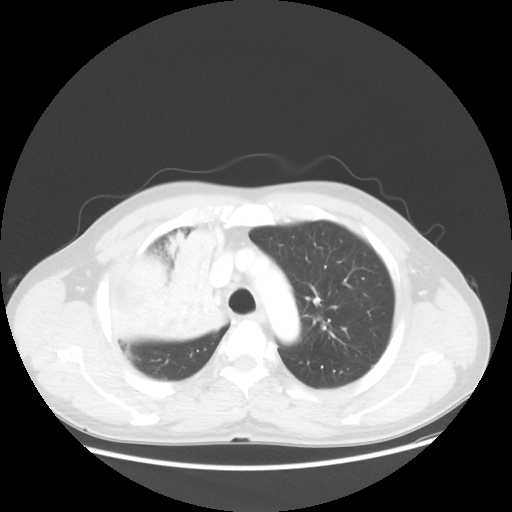
Chest CT, one axial slice; slice 41 of 56 in the series (ordered by position); 100 kVp; lung window (W 1500 / L -600 HU); 512 × 512 image matrix, field of view 398 × 398 mm. Patient: male, 60 years. From the clinical record (not read from this slice): clinical TNM (as recorded): T2a N1 M0.
Outlined on this slice (bounding box drawn by a radiologist):
- lung tumour (recorded histology: squamous cell carcinoma): box from (x=140, y=223) to (x=235, y=361) px